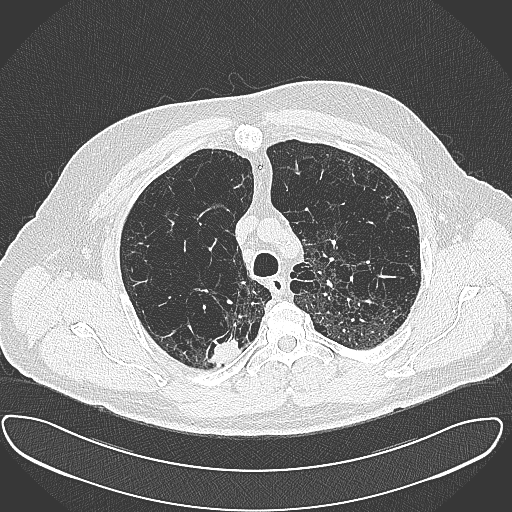
Axial slice from a low-dose chest CT screening exam, first (baseline) screen, lung window (W 1500 / L -600 HU), 1 mm slice thickness, slice 85 of 385 in the series, 512 × 512 image matrix, field of view 408 × 408 mm. Male, age 60 years at enrolment. Current smoker at enrolment.
Expert reader's lesion annotation, bounding box [x1, y1, x2, y2] px = [198, 327, 244, 368]. The exam's reader record, not a measurement of the box and not confirmed to be the same lesion: non-calcified nodule or mass ≥4 mm, right upper lobe, 15 × 25 mm, spiculated (stellate) margins, soft tissue attenuation. Official screen result: positive, change unspecified: nodule(s) >= 4 mm or enlarging nodule(s), mass(es), or other non-specific abnormalities suspicious for lung cancer. Lung cancer was diagnosed 32 days after this screen: carcinoma, NOS, right upper lobe, moderately differentiated (G2), stage IB (AJCC 6th edition), 35 mm at pathology.